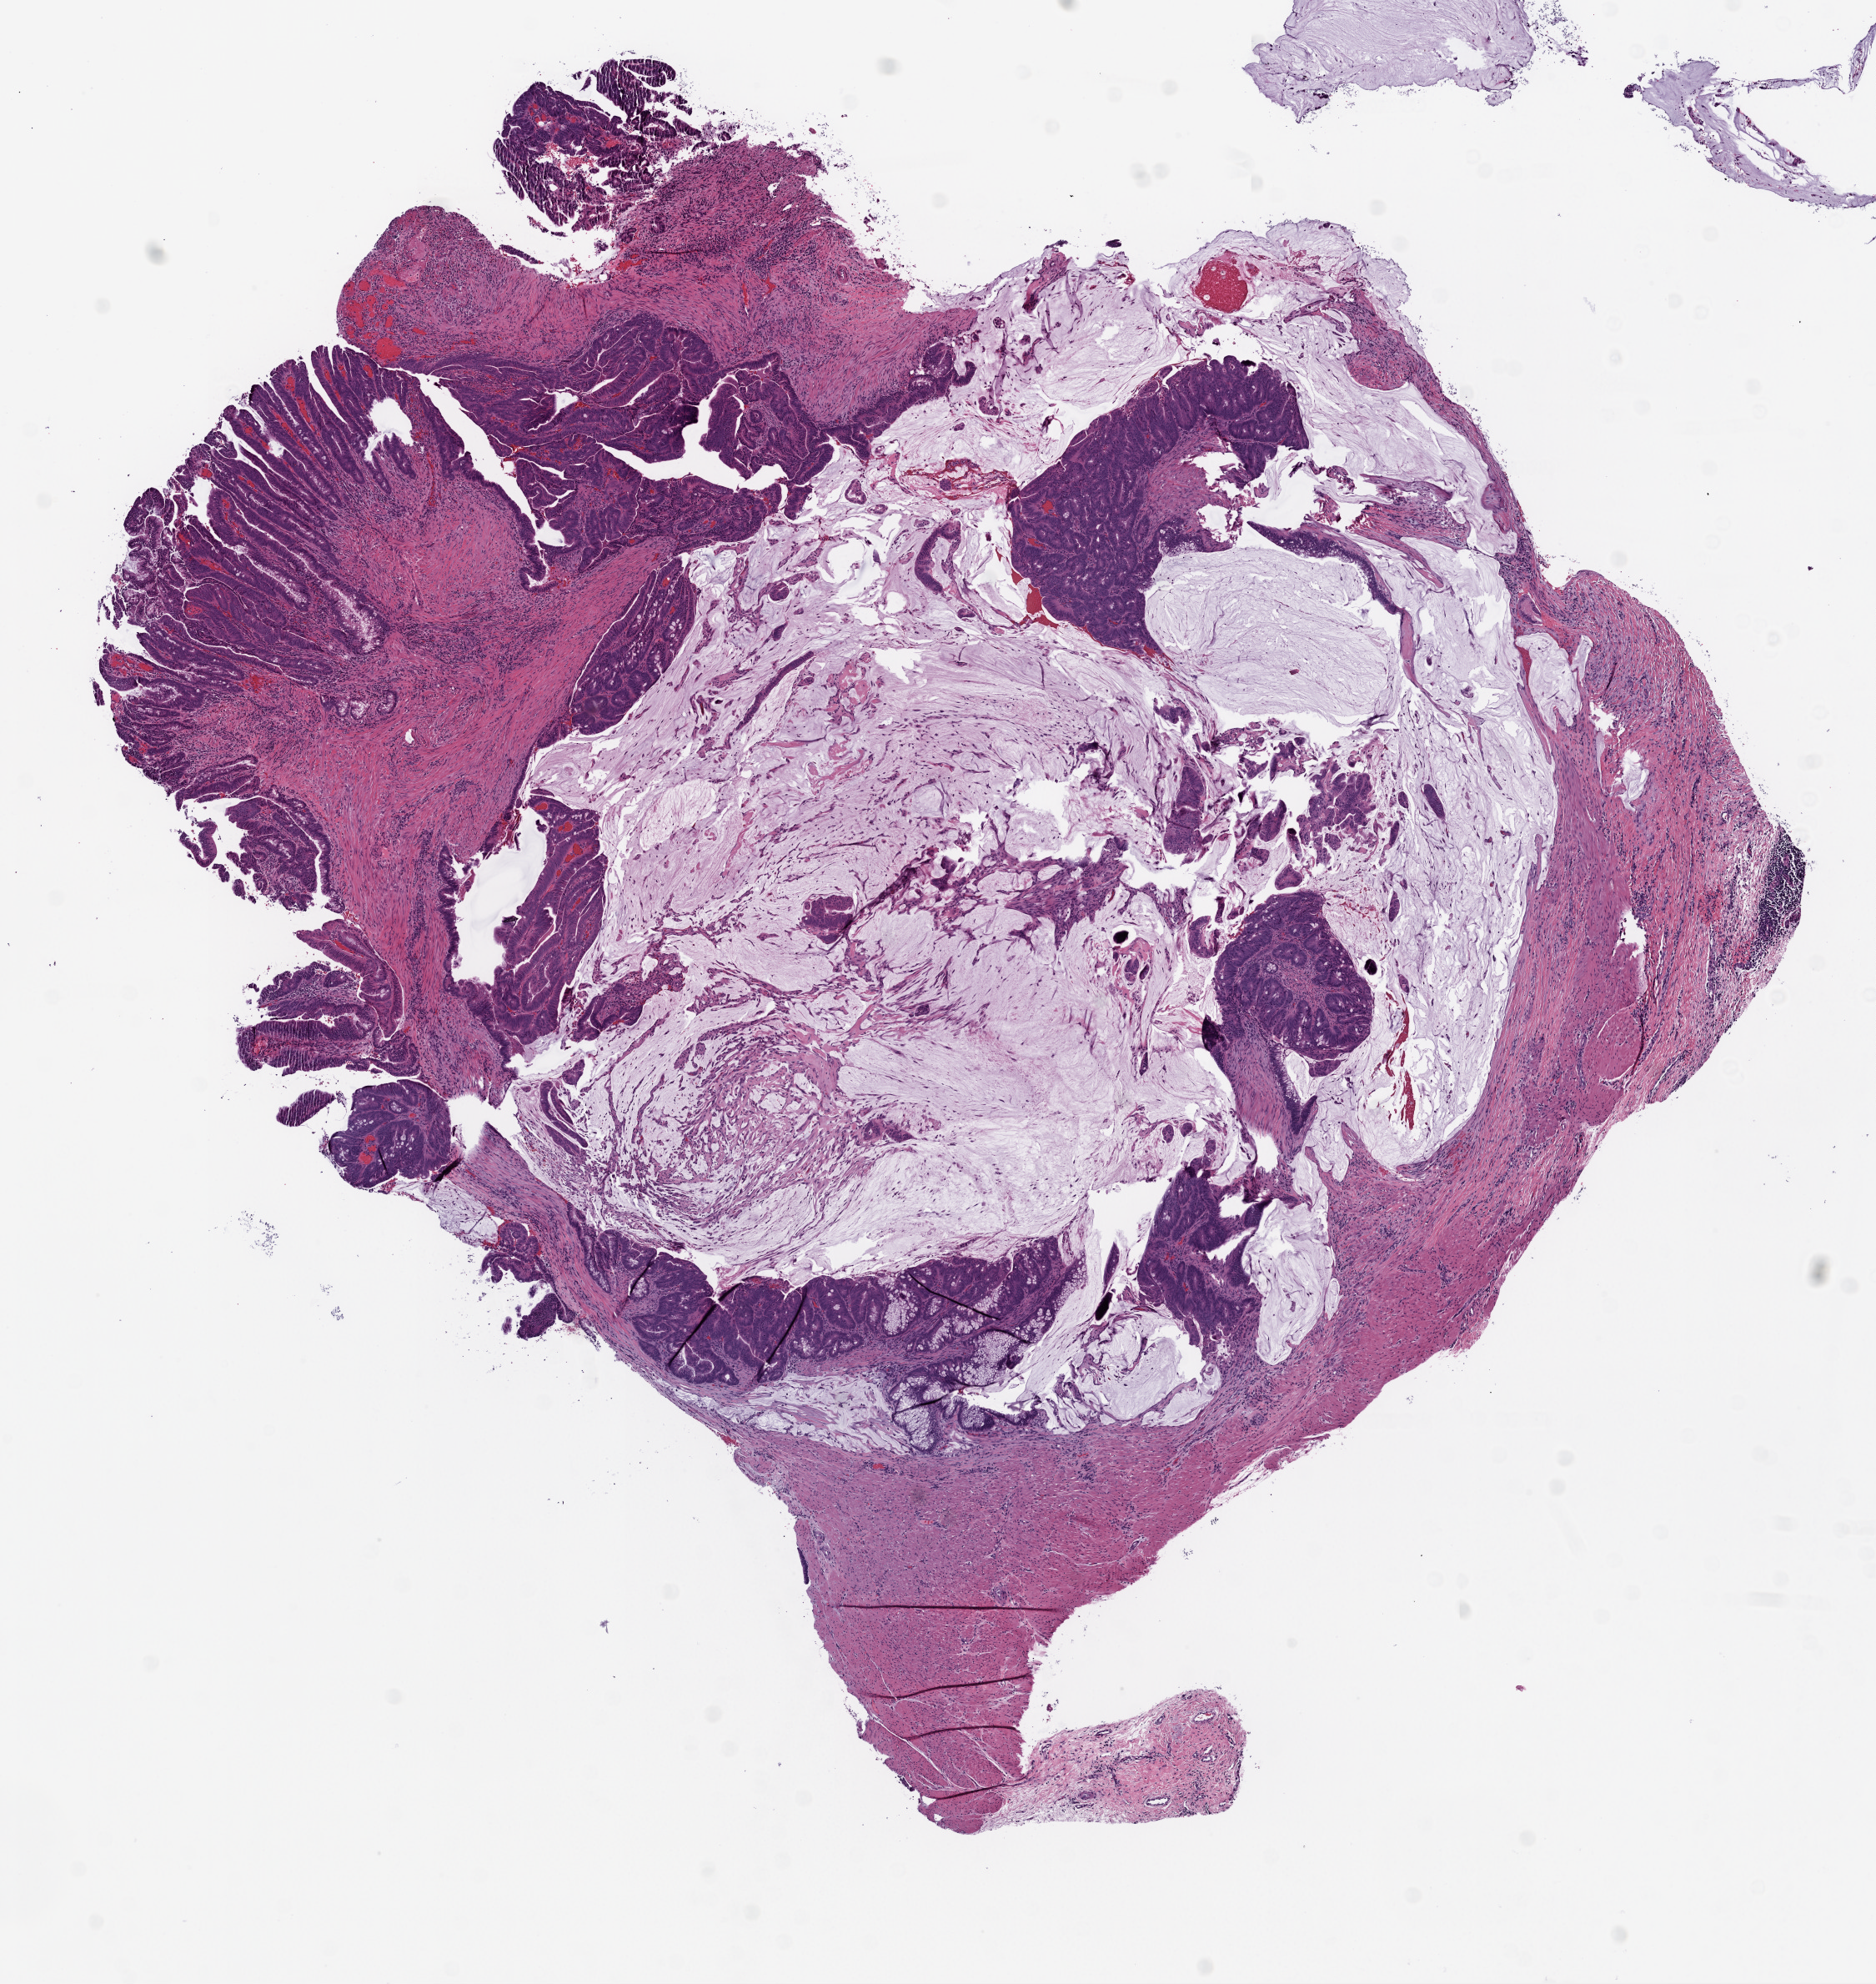
H&E-stained whole-slide image — shown as a low-resolution overview of the whole scanned area (about 9.0 x 9.5 mm, acquisition: 20x scan), frozen section from the top of the tissue portion, colon, primary tumour sample. Male, age 73 years at initial diagnosis. Composition of this section per pathologist review: tumour nuclei 85%, normal cells 0%, stromal cells 30%, necrosis 0%.
Histologic diagnosis: Adenocarcinoma, NOS. AJCC pathologic stage: IIA.